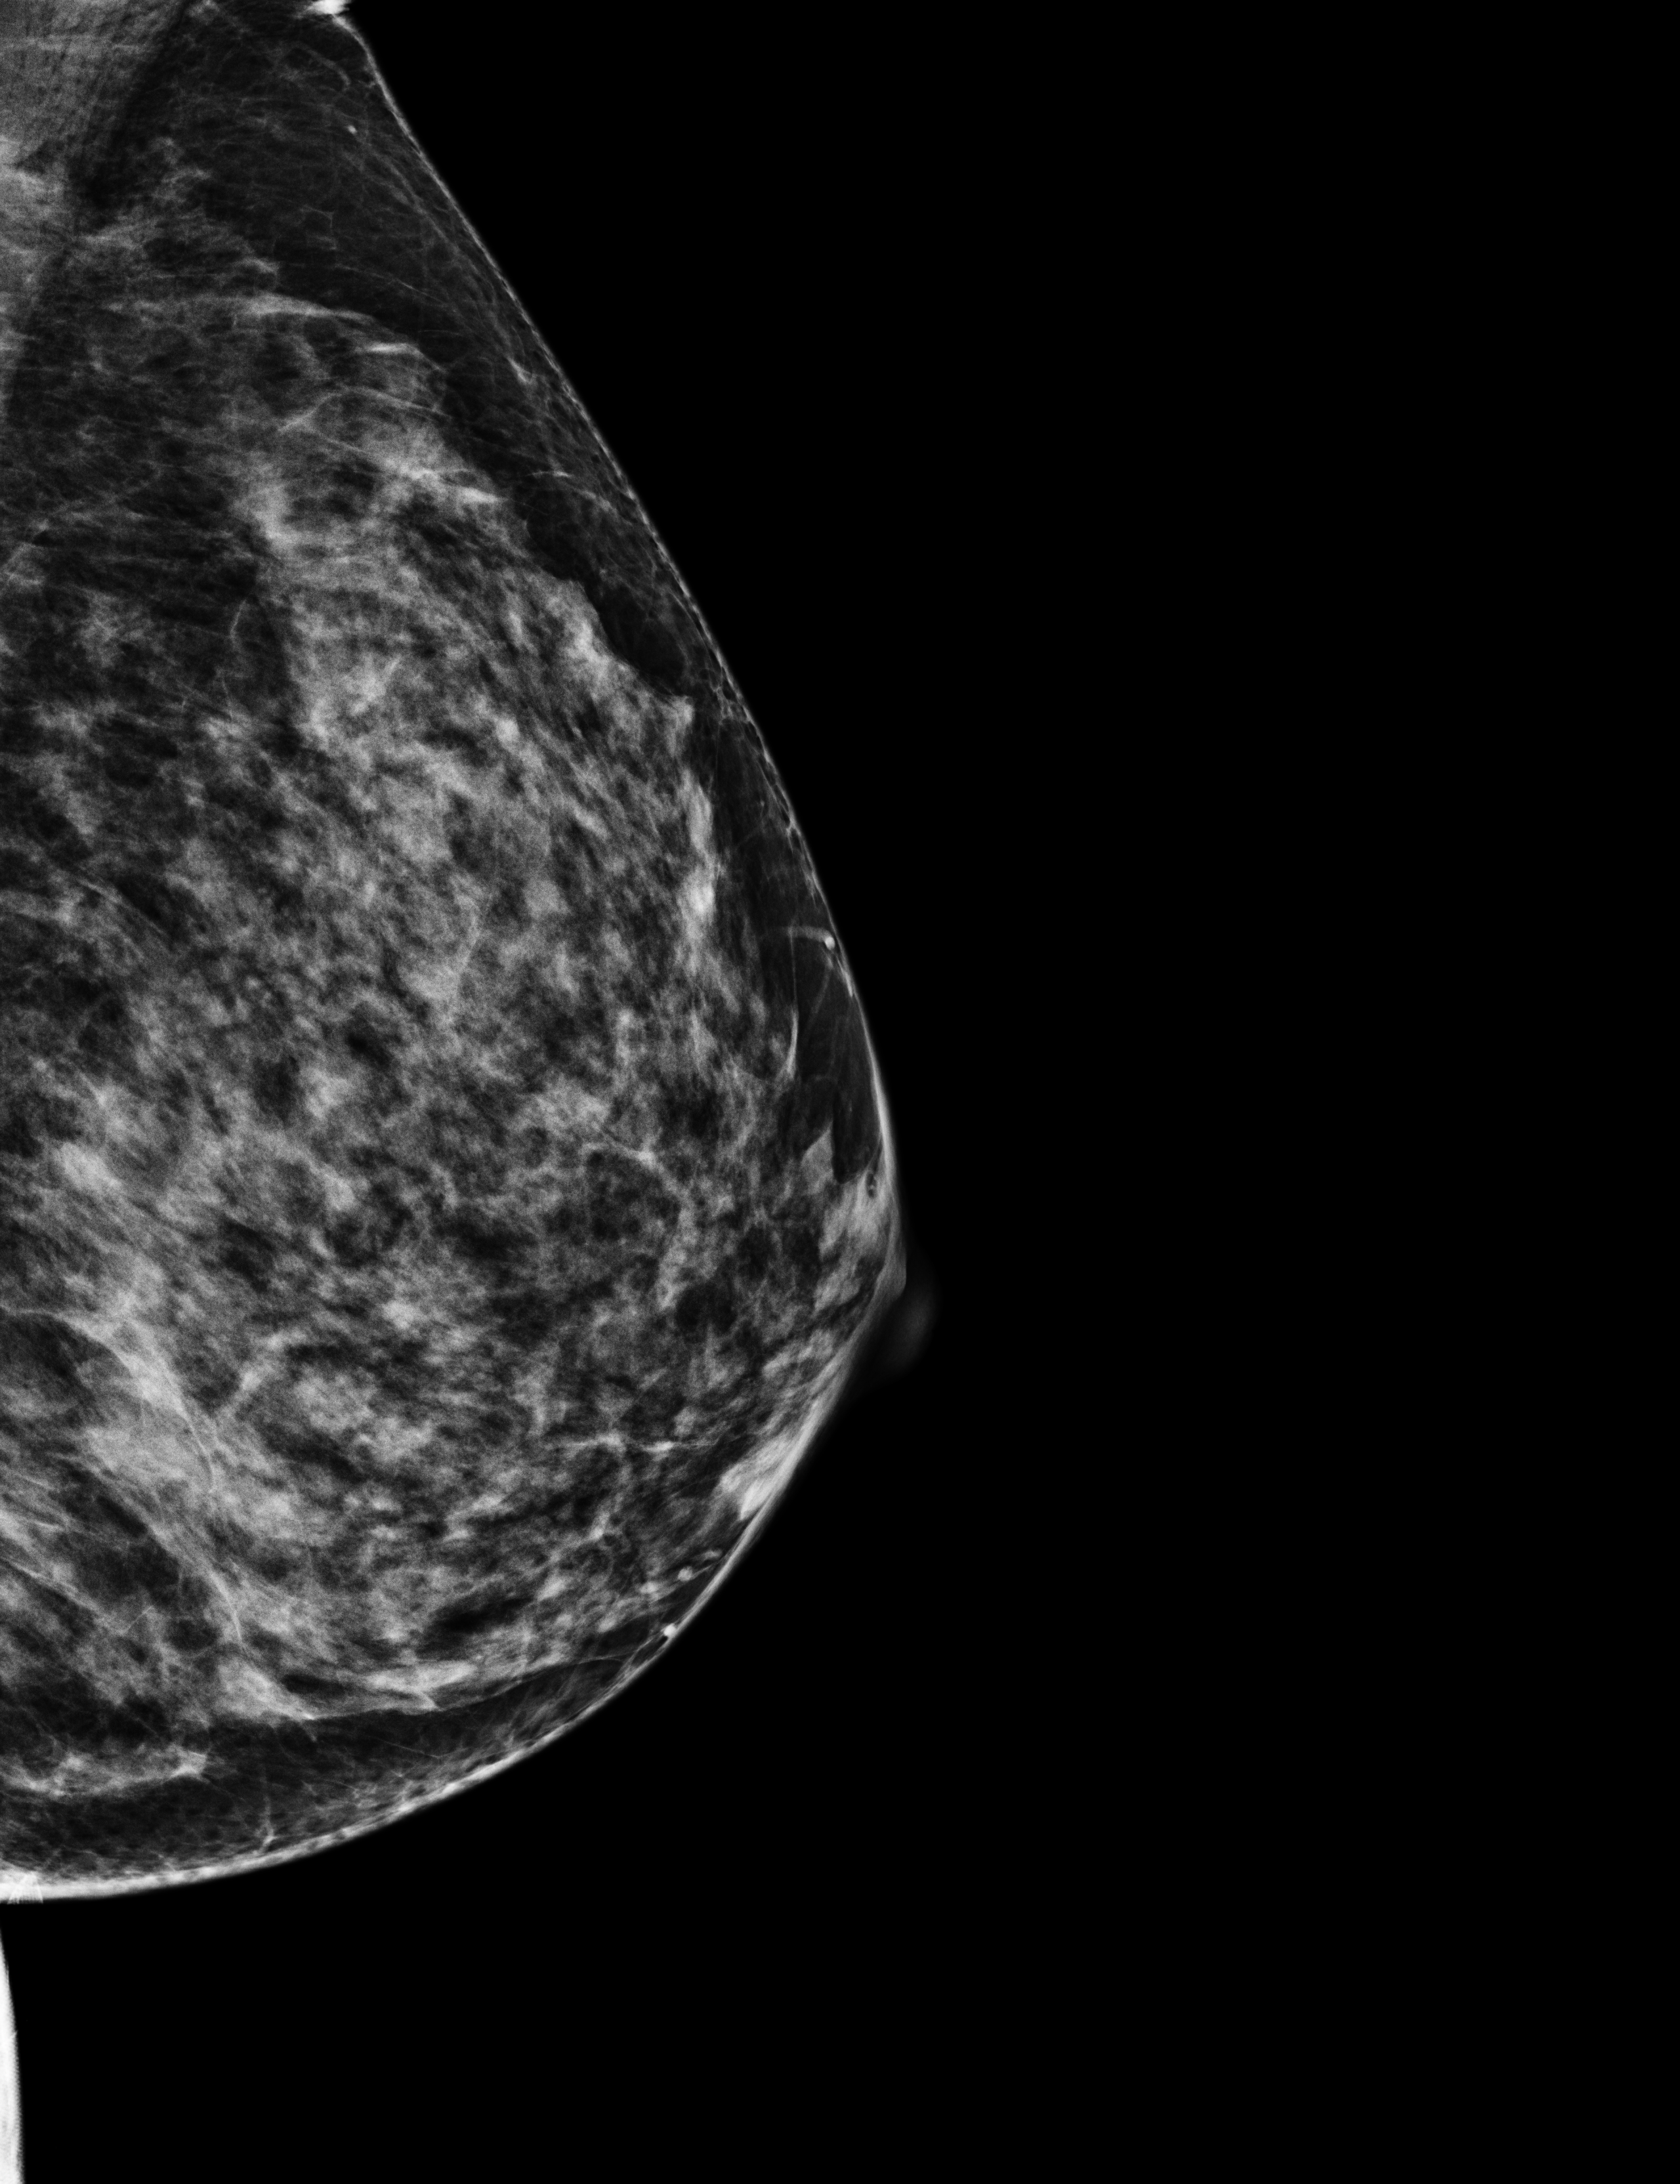
Screening examination; compressed breast thickness 50 mm; system: Selenia Dimensions. Patient aged 50 years (female).
Image type: full-field digital mammogram. Breast: left. Projection: exaggerated CC view (lateral).